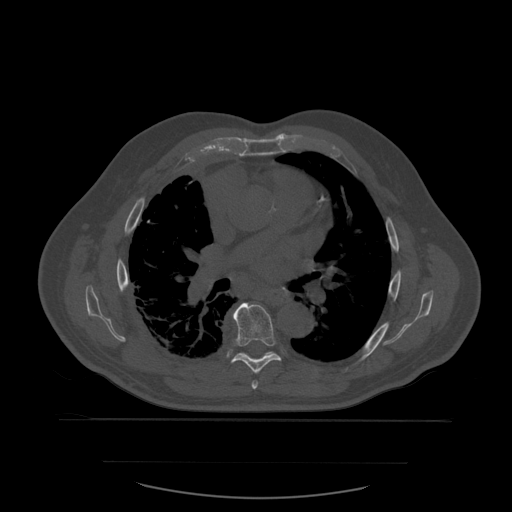
CT including the spine, one axial slice. Position 382 of 590 along the scan axis. Bone window (W 1800 / L 400 HU). 512 × 512 image matrix, field of view 479 × 479 mm. Patient age 71 years. Case-level facts recorded for this patient, not image findings: primary cancer: lung.
Structures marked on this image (semi-automatically segmented with operator editing):
- T6 vertebra: bounding box (x1, y1, x2, y2) in pixels: (252, 381, 259, 390)
- T7 vertebra: (231, 303, 282, 374)